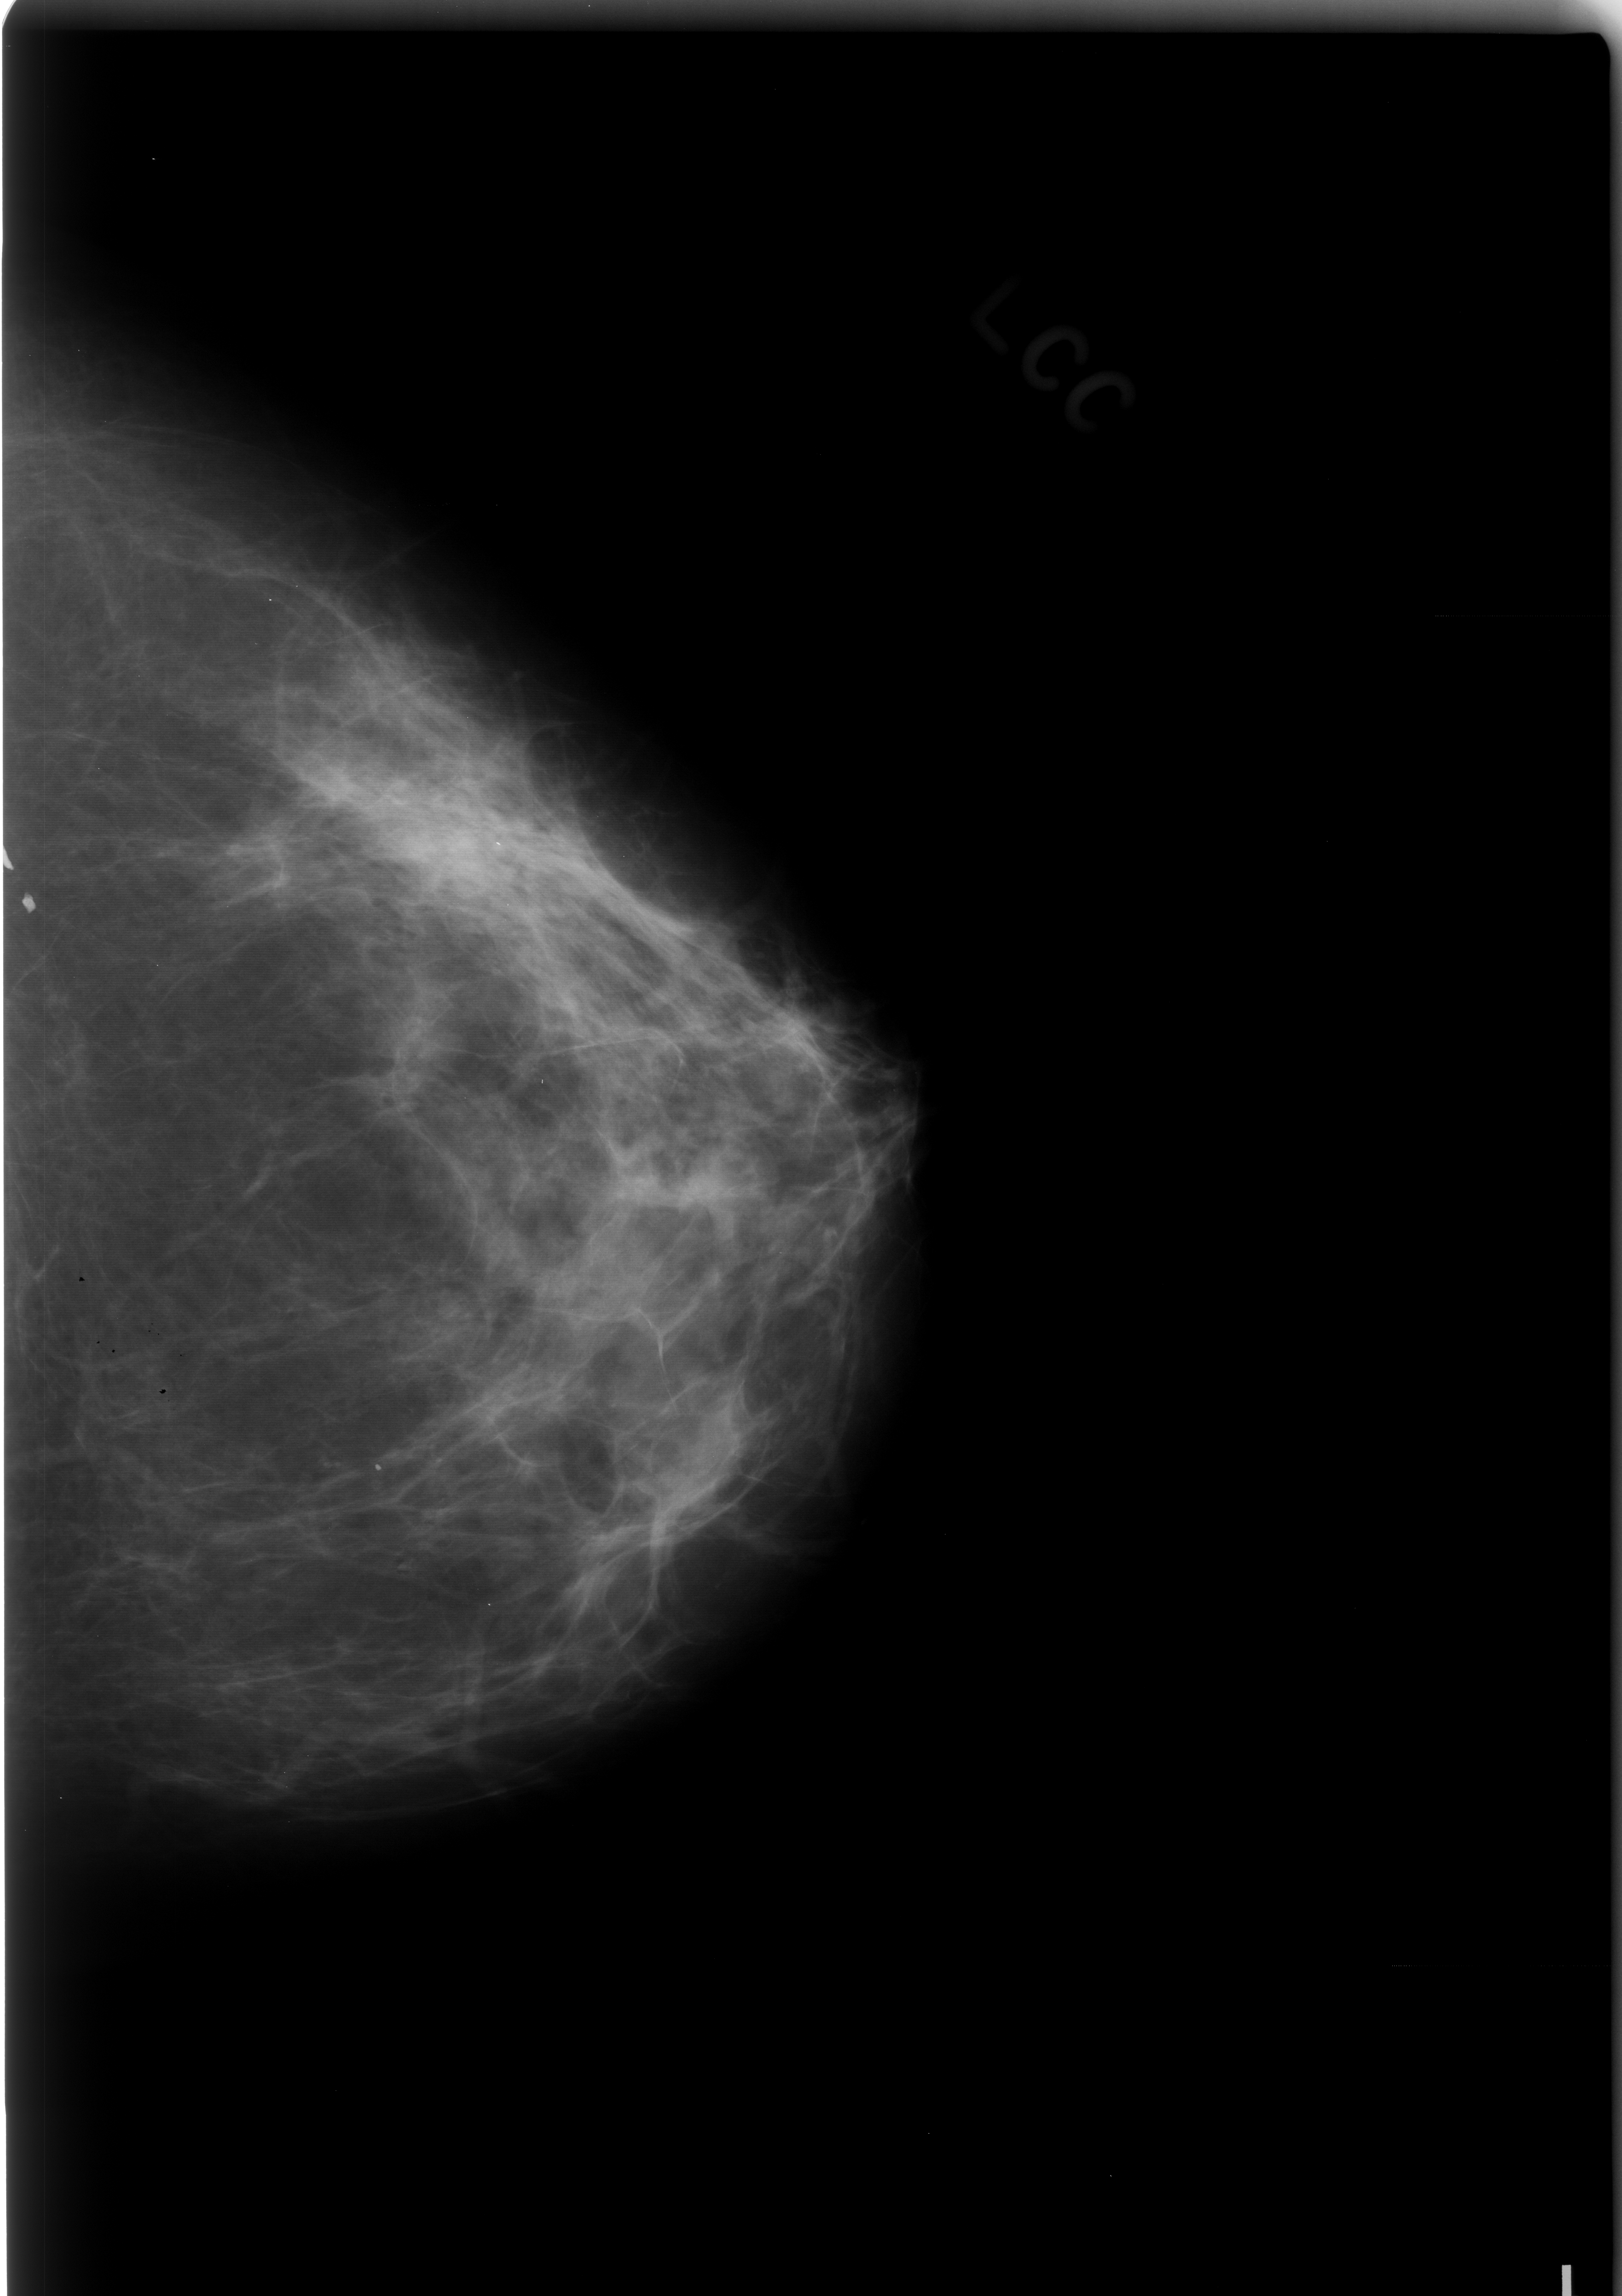
Scanned film-screen mammogram; left breast; CC view; BI-RADS breast density category 2 (scale 1–4).
Marked abnormality: calcifications, morphology lucent centered, distribution linear; BI-RADS assessment category 2; pathology result (as recorded, not read from the image): benign.